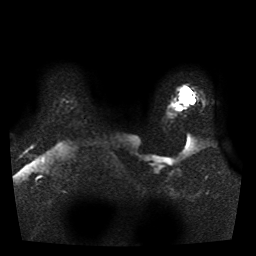
Breast MRI, one axial slice; slice 32 of 41 in the series (ordered by position); diffusion-weighted series; image 2 of 3 stored at this slice position (different b-values; order by instance number); 1.5 T; 5 mm slice thickness; 256 × 256 image matrix, field of view 330 × 330 mm. Female patient.
Structures marked on this image (outlined manually by an expert reader):
- tumour on diffusion-weighted imaging: box from (x=180, y=95) to (x=194, y=108) px